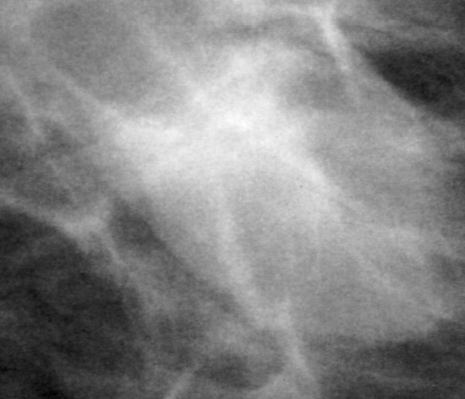
Cropped region of a digitized screen-film mammogram centred on a radiologist-marked abnormality; right breast; MLO view.
Finding: mass, shape oval, margins circumscribed; BI-RADS assessment category 4; pathology result (as recorded, not read from the image): benign.